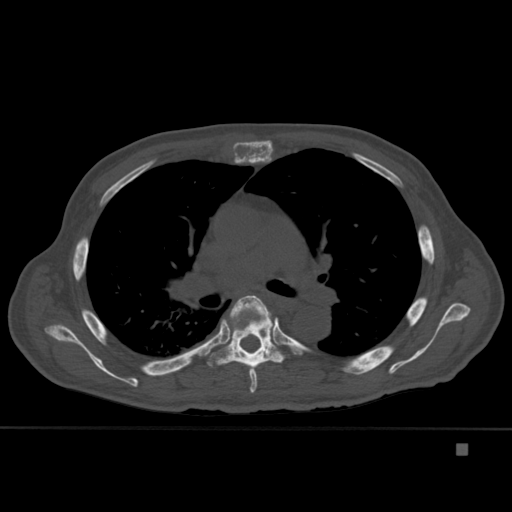
CT including the spine, one axial slice. Position 297 of 451 along the scan axis. Bone window (W 1800 / L 400 HU). 1.5 mm slice thickness. 512 × 512 image matrix, field of view 378 × 378 mm. Patient: male, 75 years. Case-level facts recorded for this patient, not image findings: primary cancer: prostate.
Outlined on this slice (semi-automatically segmented with operator editing):
- T5 vertebra: bounding box (x1, y1, x2, y2) in pixels: (222, 295, 279, 393)
- T6 vertebra: (207, 311, 286, 368)